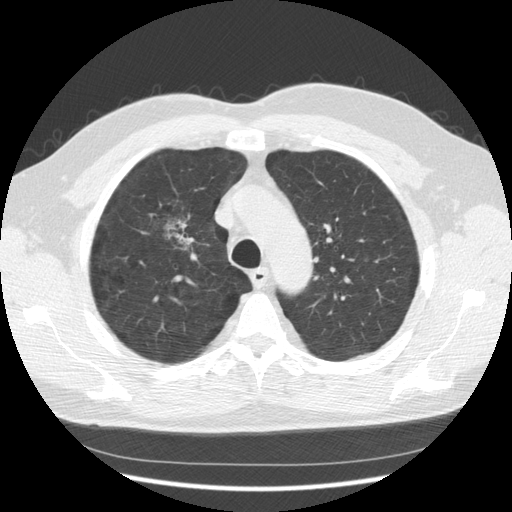
Axial slice from a low-dose chest CT screening exam; third annual screen; lung window (W 1500 / L -600 HU); 2.5 mm slice thickness; slice 94 of 133 in the series. Male participant, aged 60 years at enrolment. Former smoker at enrolment.
- Lesion marked by an expert reader, box from (x=140, y=199) to (x=202, y=269) px.
- Reader record for this screening exam (exam-level; its link to the box is not recorded): non-calcified nodule or mass ≥4 mm, right upper lobe, poorly defined margins, mixed attenuation, pre-existing on the prior screen: yes; interval growth: yes.
- Later outcome: lung cancer diagnosed 121 days after this screen — papillary adenocarcinoma, NOS, right upper lobe, moderately differentiated (G2), stage IB (AJCC 6th edition), 32 mm at pathology.